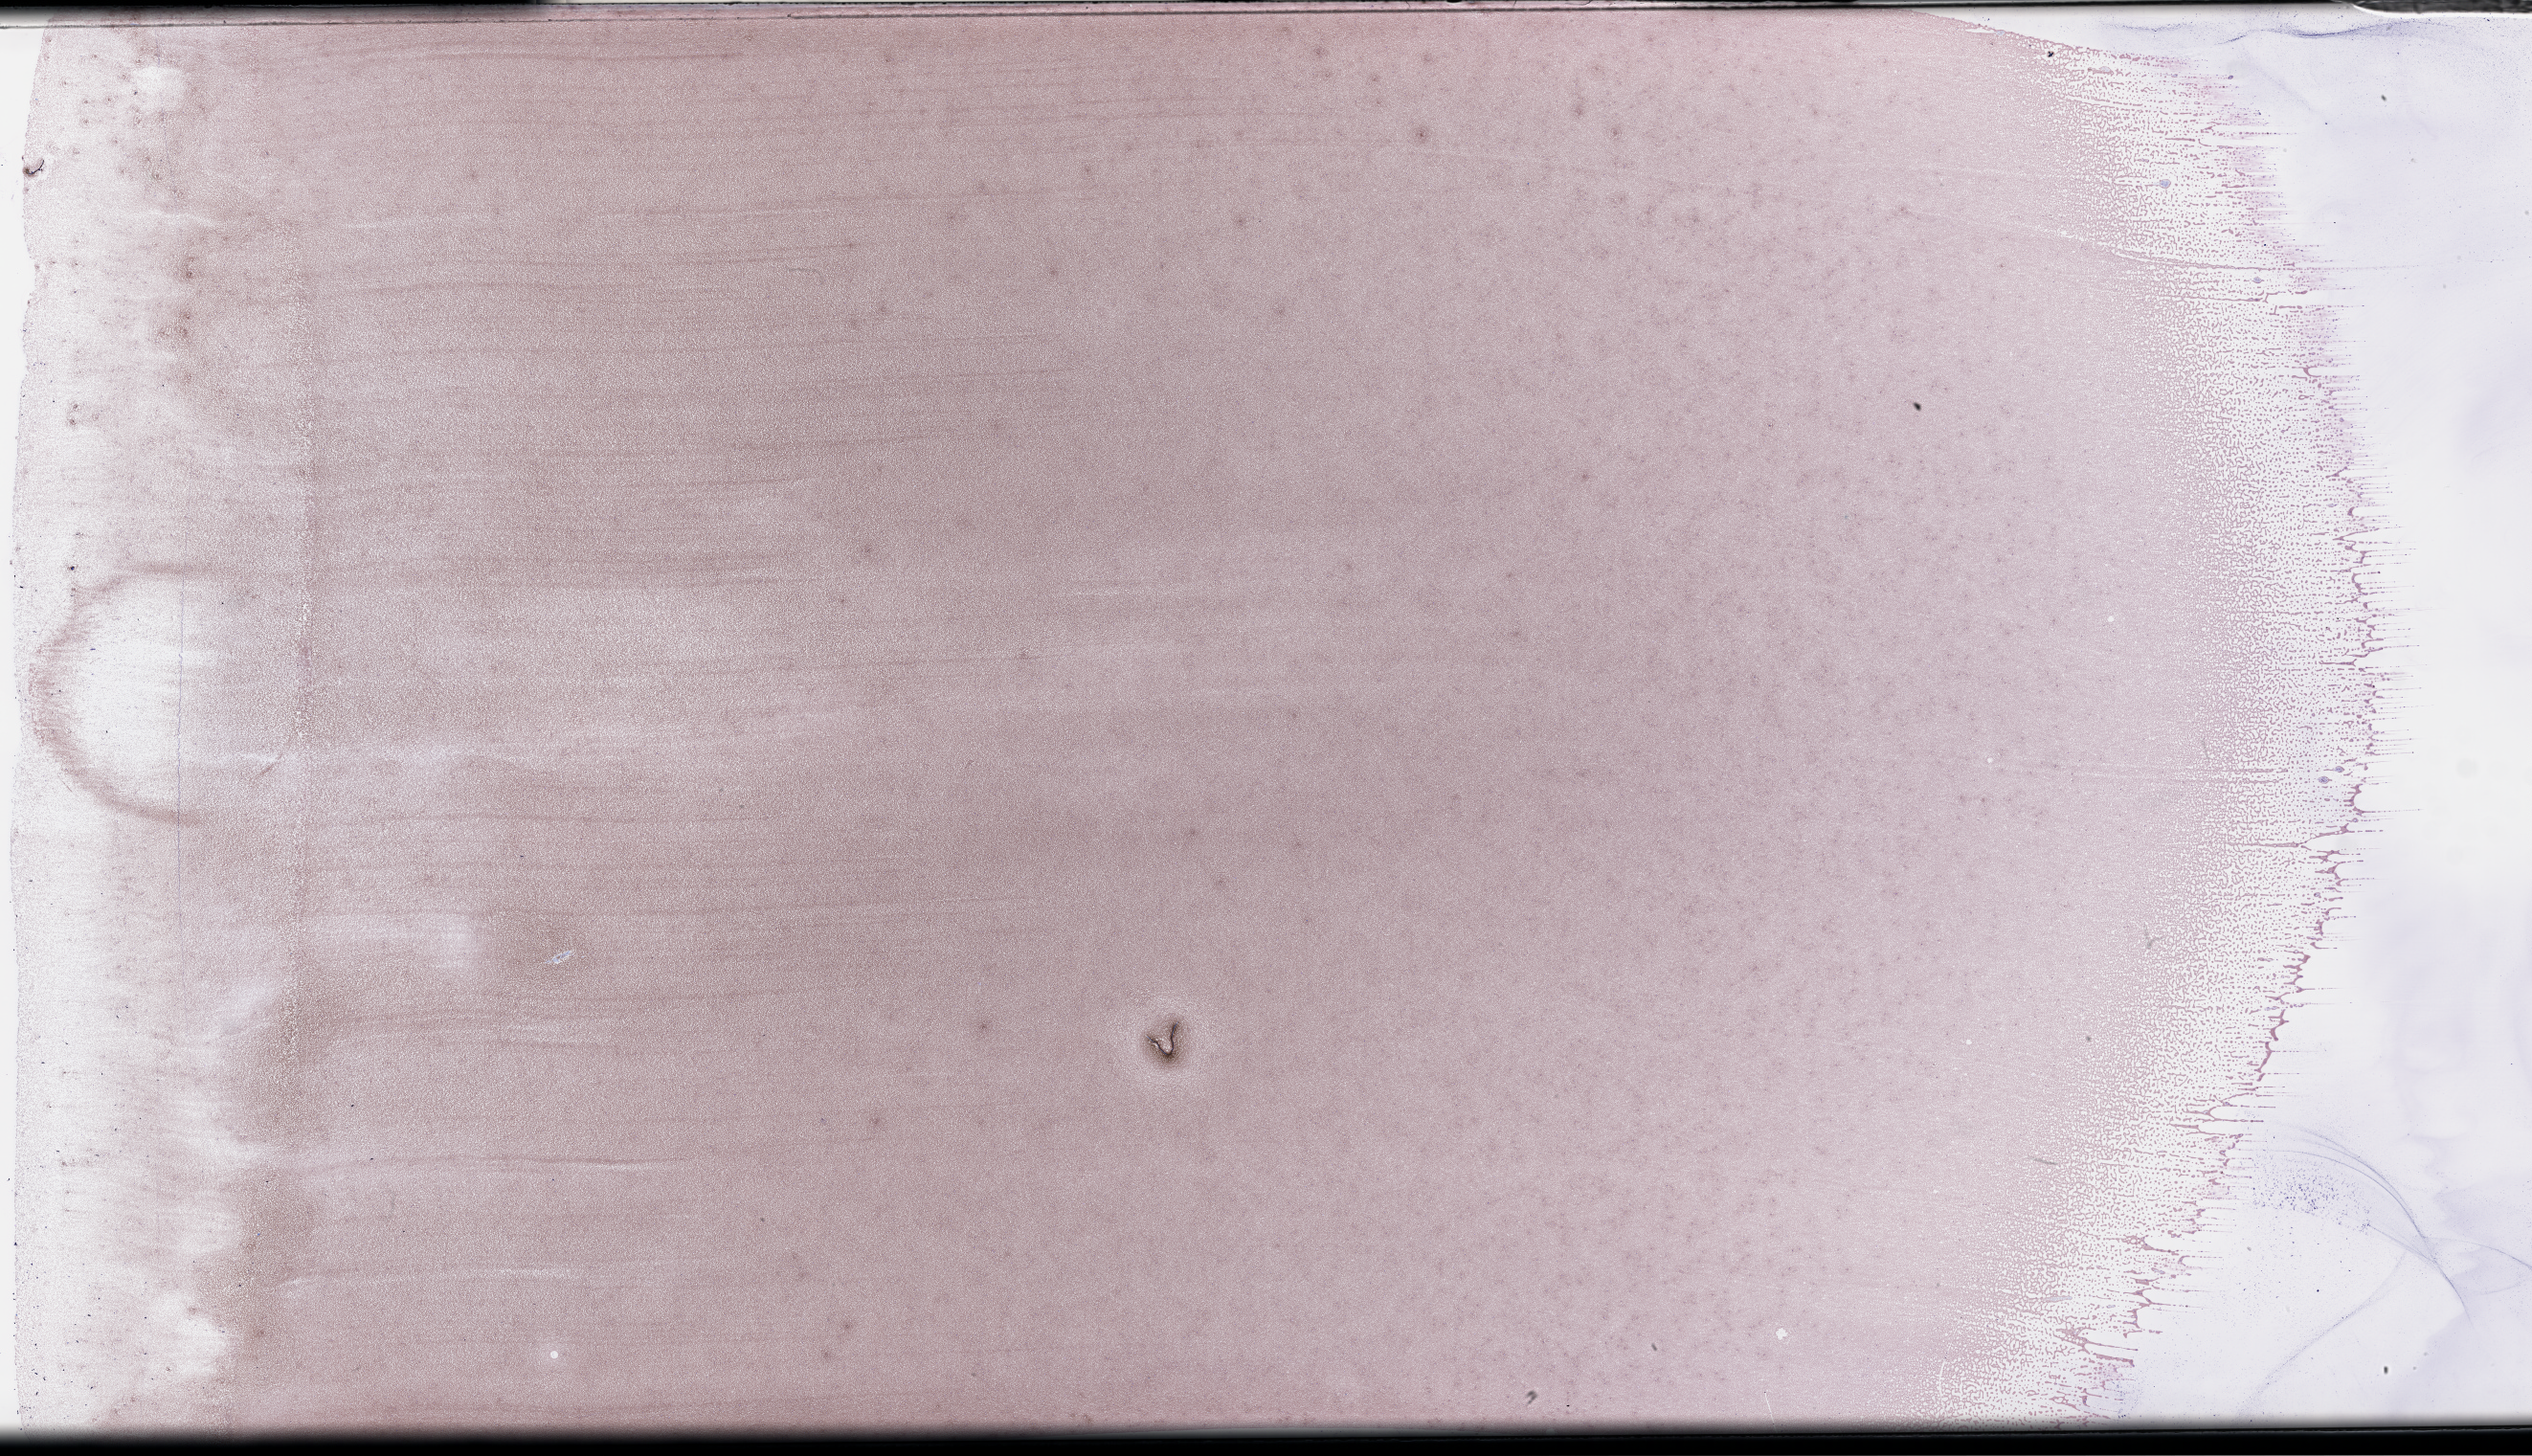
Wright-Giemsa-stained whole blood smear, whole-slide image — low-resolution overview of the scanned area, about 42.7 x 24.6 mm; EDTA-anticoagulated smear; specimen time point: collected on treatment. Patient sex: male.
From a patient with: Plasma Cell Myeloma.